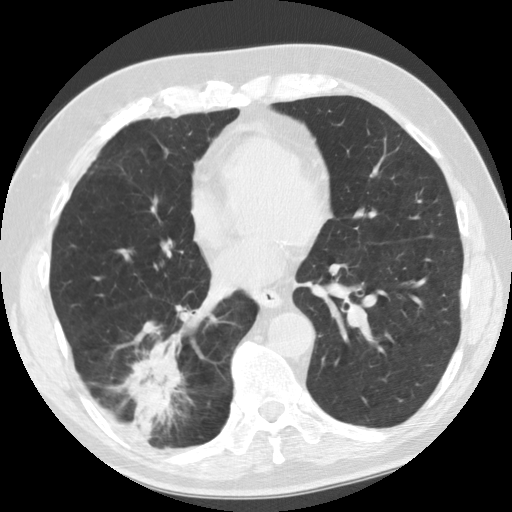
Low-dose screening chest CT, one axial slice. Slice 51 of 135 in the series (ordered by position). Reconstruction kernel STANDARD. 120 kVp. Lung window (W 1500 / L -600 HU). 512 × 512 image matrix, field of view 340 × 340 mm.
Outlined on this slice (manually delineated by an expert):
- lesion 1 (tumor, lower lobe of right lung): bounding box (x1, y1, x2, y2) in pixels: (118, 333, 184, 439)